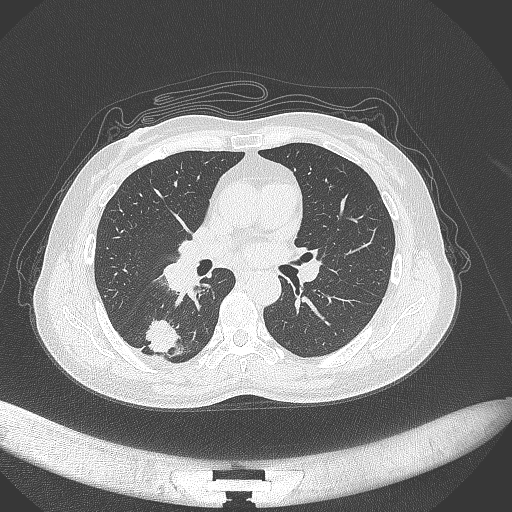
Chest CT, one axial slice; slice 165 of 352 in the series (ordered by position); reconstruction kernel B70f; 120 kVp; lung window (W 1500 / L -600 HU); 1 mm slice thickness; 512 × 512 image matrix, field of view 400 × 400 mm. Patient: female, 55 years. From the clinical record (not read from this slice): clinical TNM (as recorded): T1c N1 M0.
Annotated regions visible in this slice (bounding box drawn by a radiologist):
- lung tumour (recorded histology: adenocarcinoma): bounding box [x1, y1, x2, y2] px = [142, 316, 185, 357]